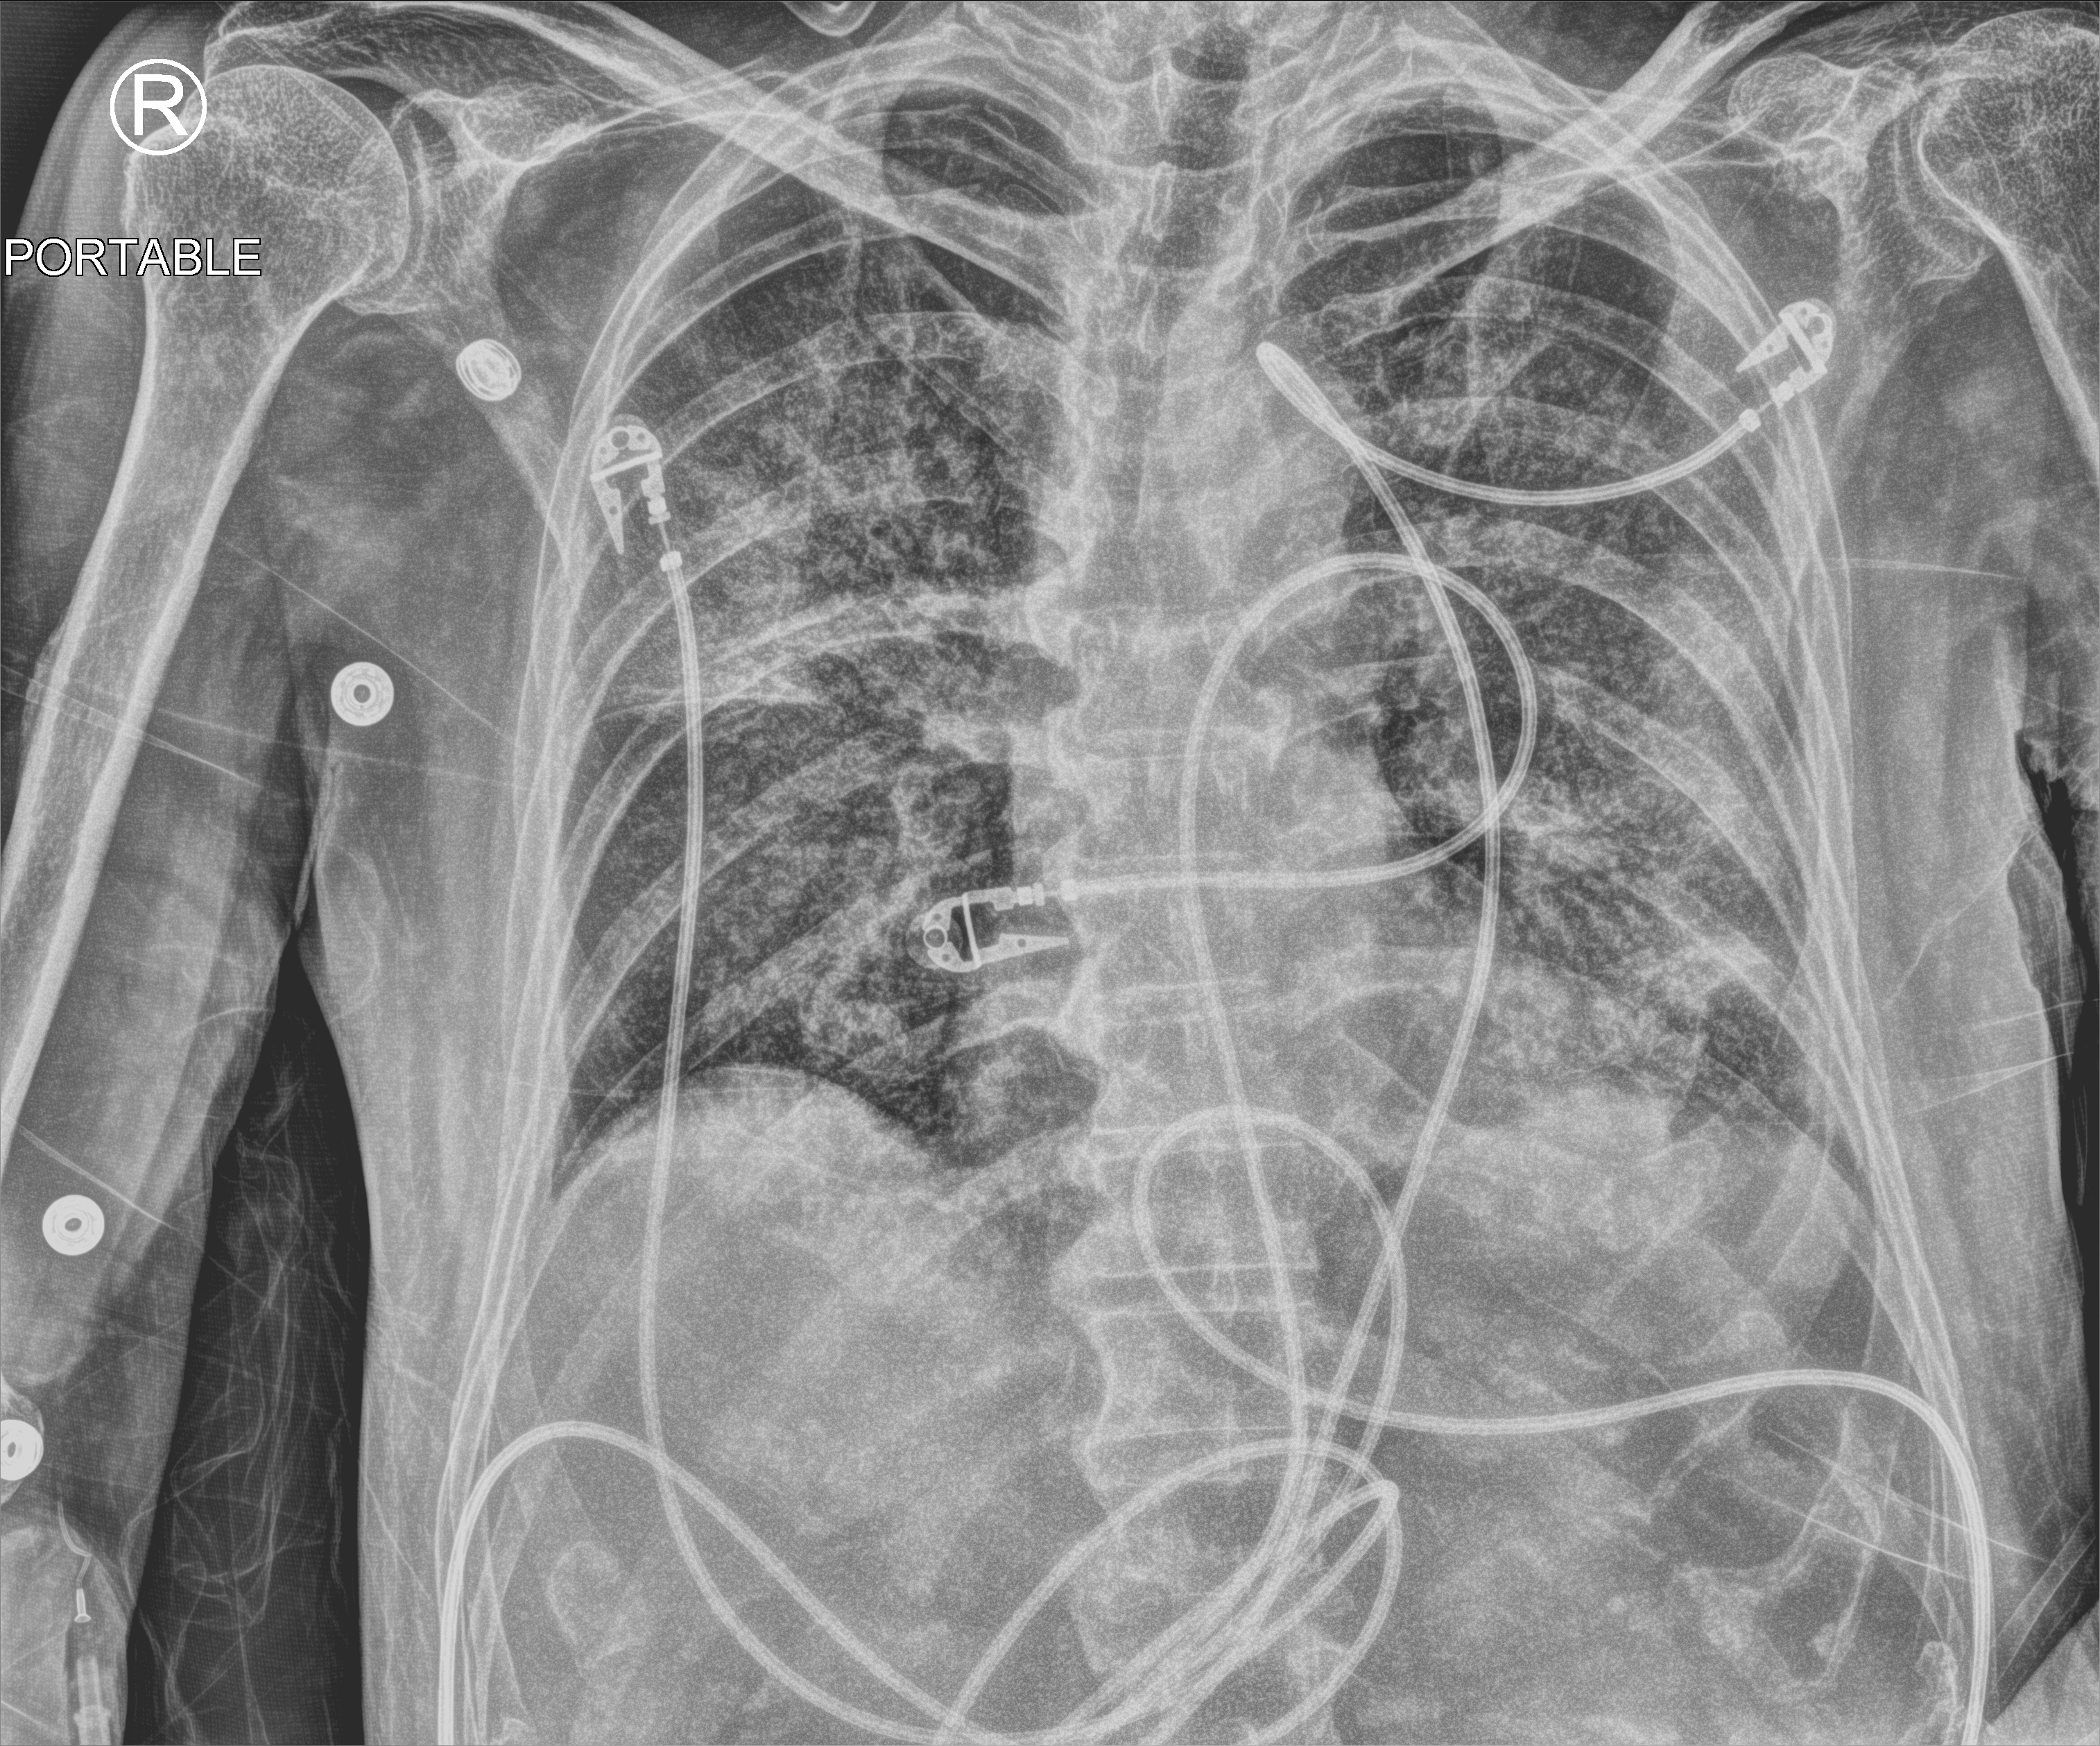
Chest X-ray (portable), anteroposterior (AP) projection. Patient hospitalised with COVID-19; male, aged 60–74 years.
From the hospital-stay record, not from the radiograph (when in the stay this image was taken is not recorded):
- admitted to intensive care during this hospital stay: yes
- mechanically ventilated during this hospital stay: yes
- smoking status (admission record): current